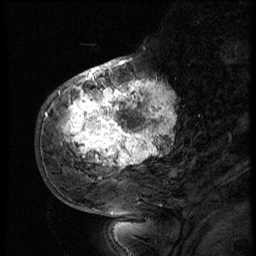
Breast MRI (dynamic contrast-enhanced), one sagittal slice. Slice 20 of 56 in the series (ordered by position). 3 images stored at this slice position (order not interpretable as contrast timing). 1.5 T. TE 4.2 ms, TR 9 ms. 2.5 mm slice thickness. 256 × 256 image matrix. Patient: female, 51 years. Case-level facts recorded for this patient, not image findings: setting: breast cancer imaged before/during neoadjuvant chemotherapy; receptor status: triple-negative.
Annotated regions visible in this slice (semi-automatically segmented with operator editing):
- analysis volume of interest (the breast-tissue region the enhancement analysis was run in; not a lesion): bounding box <52,66,183,179> (left, top, right, bottom; pixels)
- tumour enhancement mask (voxels above the 140 % enhancement threshold inside the analysis volume of interest): <62,72,175,171>